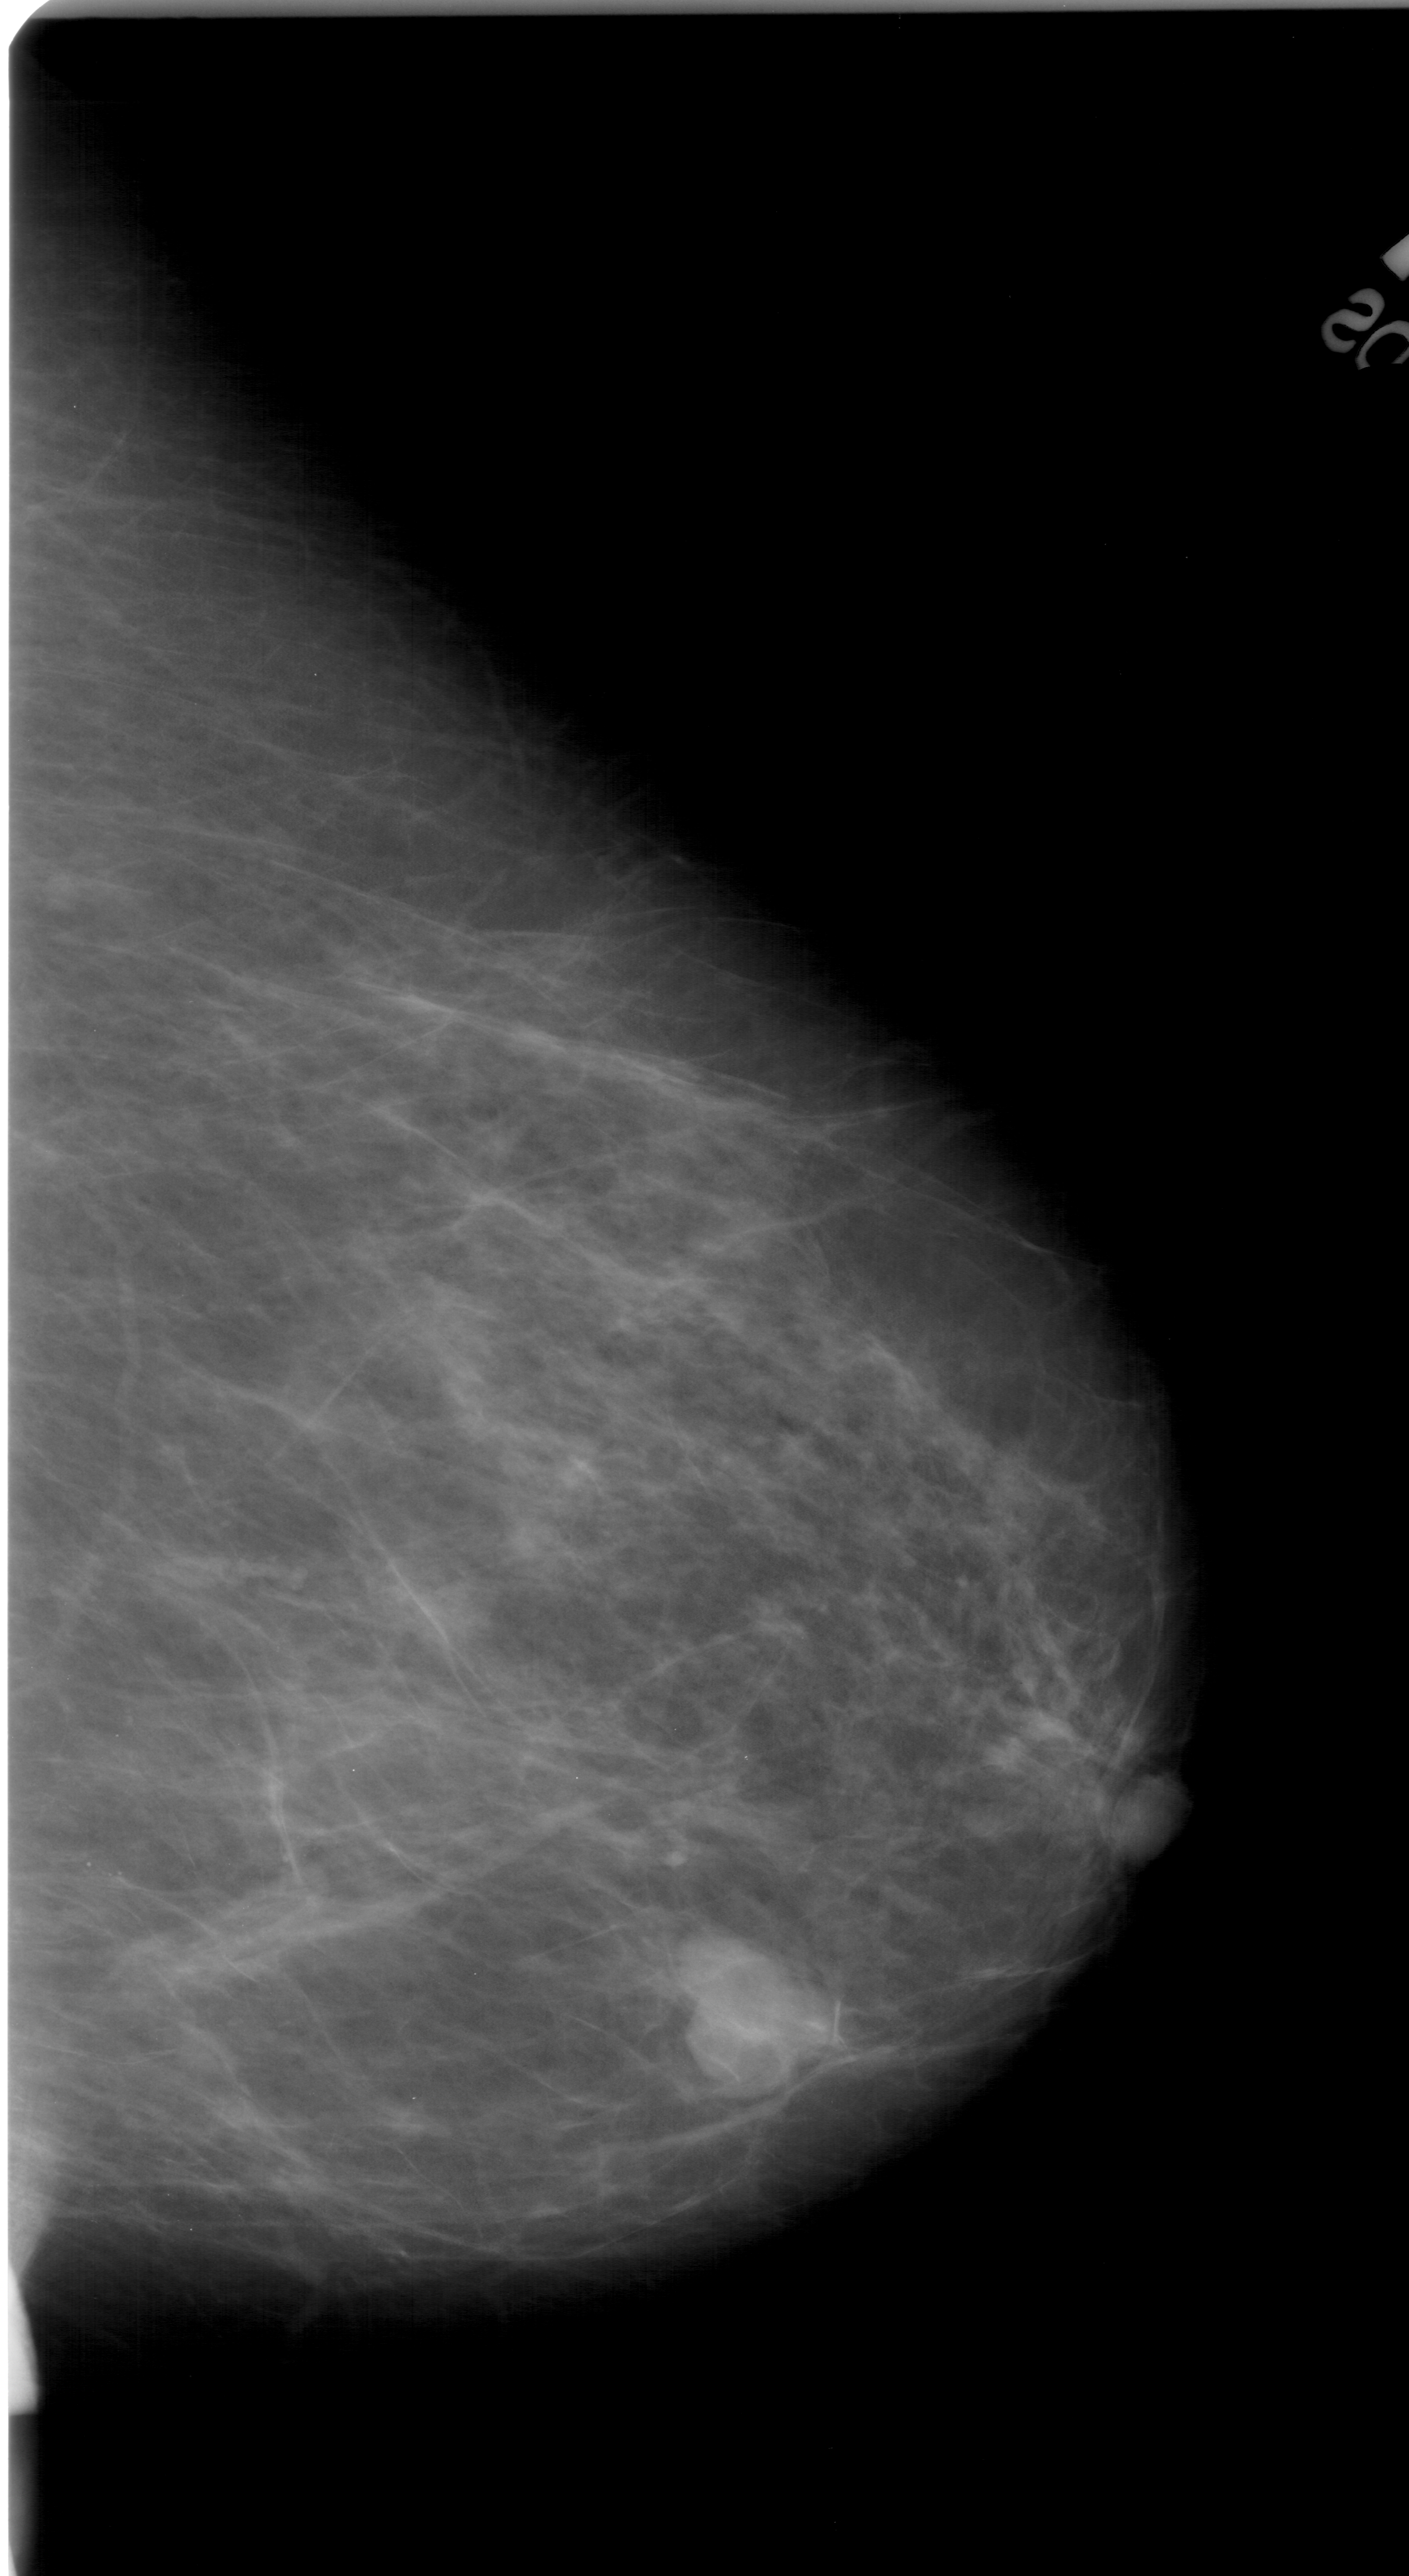
Scanned film-screen mammogram; right breast; CC view; BI-RADS breast density category 3 (scale 1–4); 1409 × 2576 image matrix.
Marked abnormalities (boxes around the expert regions of interest):
- mass, shape lobulated, margins circumscribed; BI-RADS assessment category 4; pathology result (as recorded, not read from the image): benign: box from (x=677, y=1929) to (x=830, y=2083) px